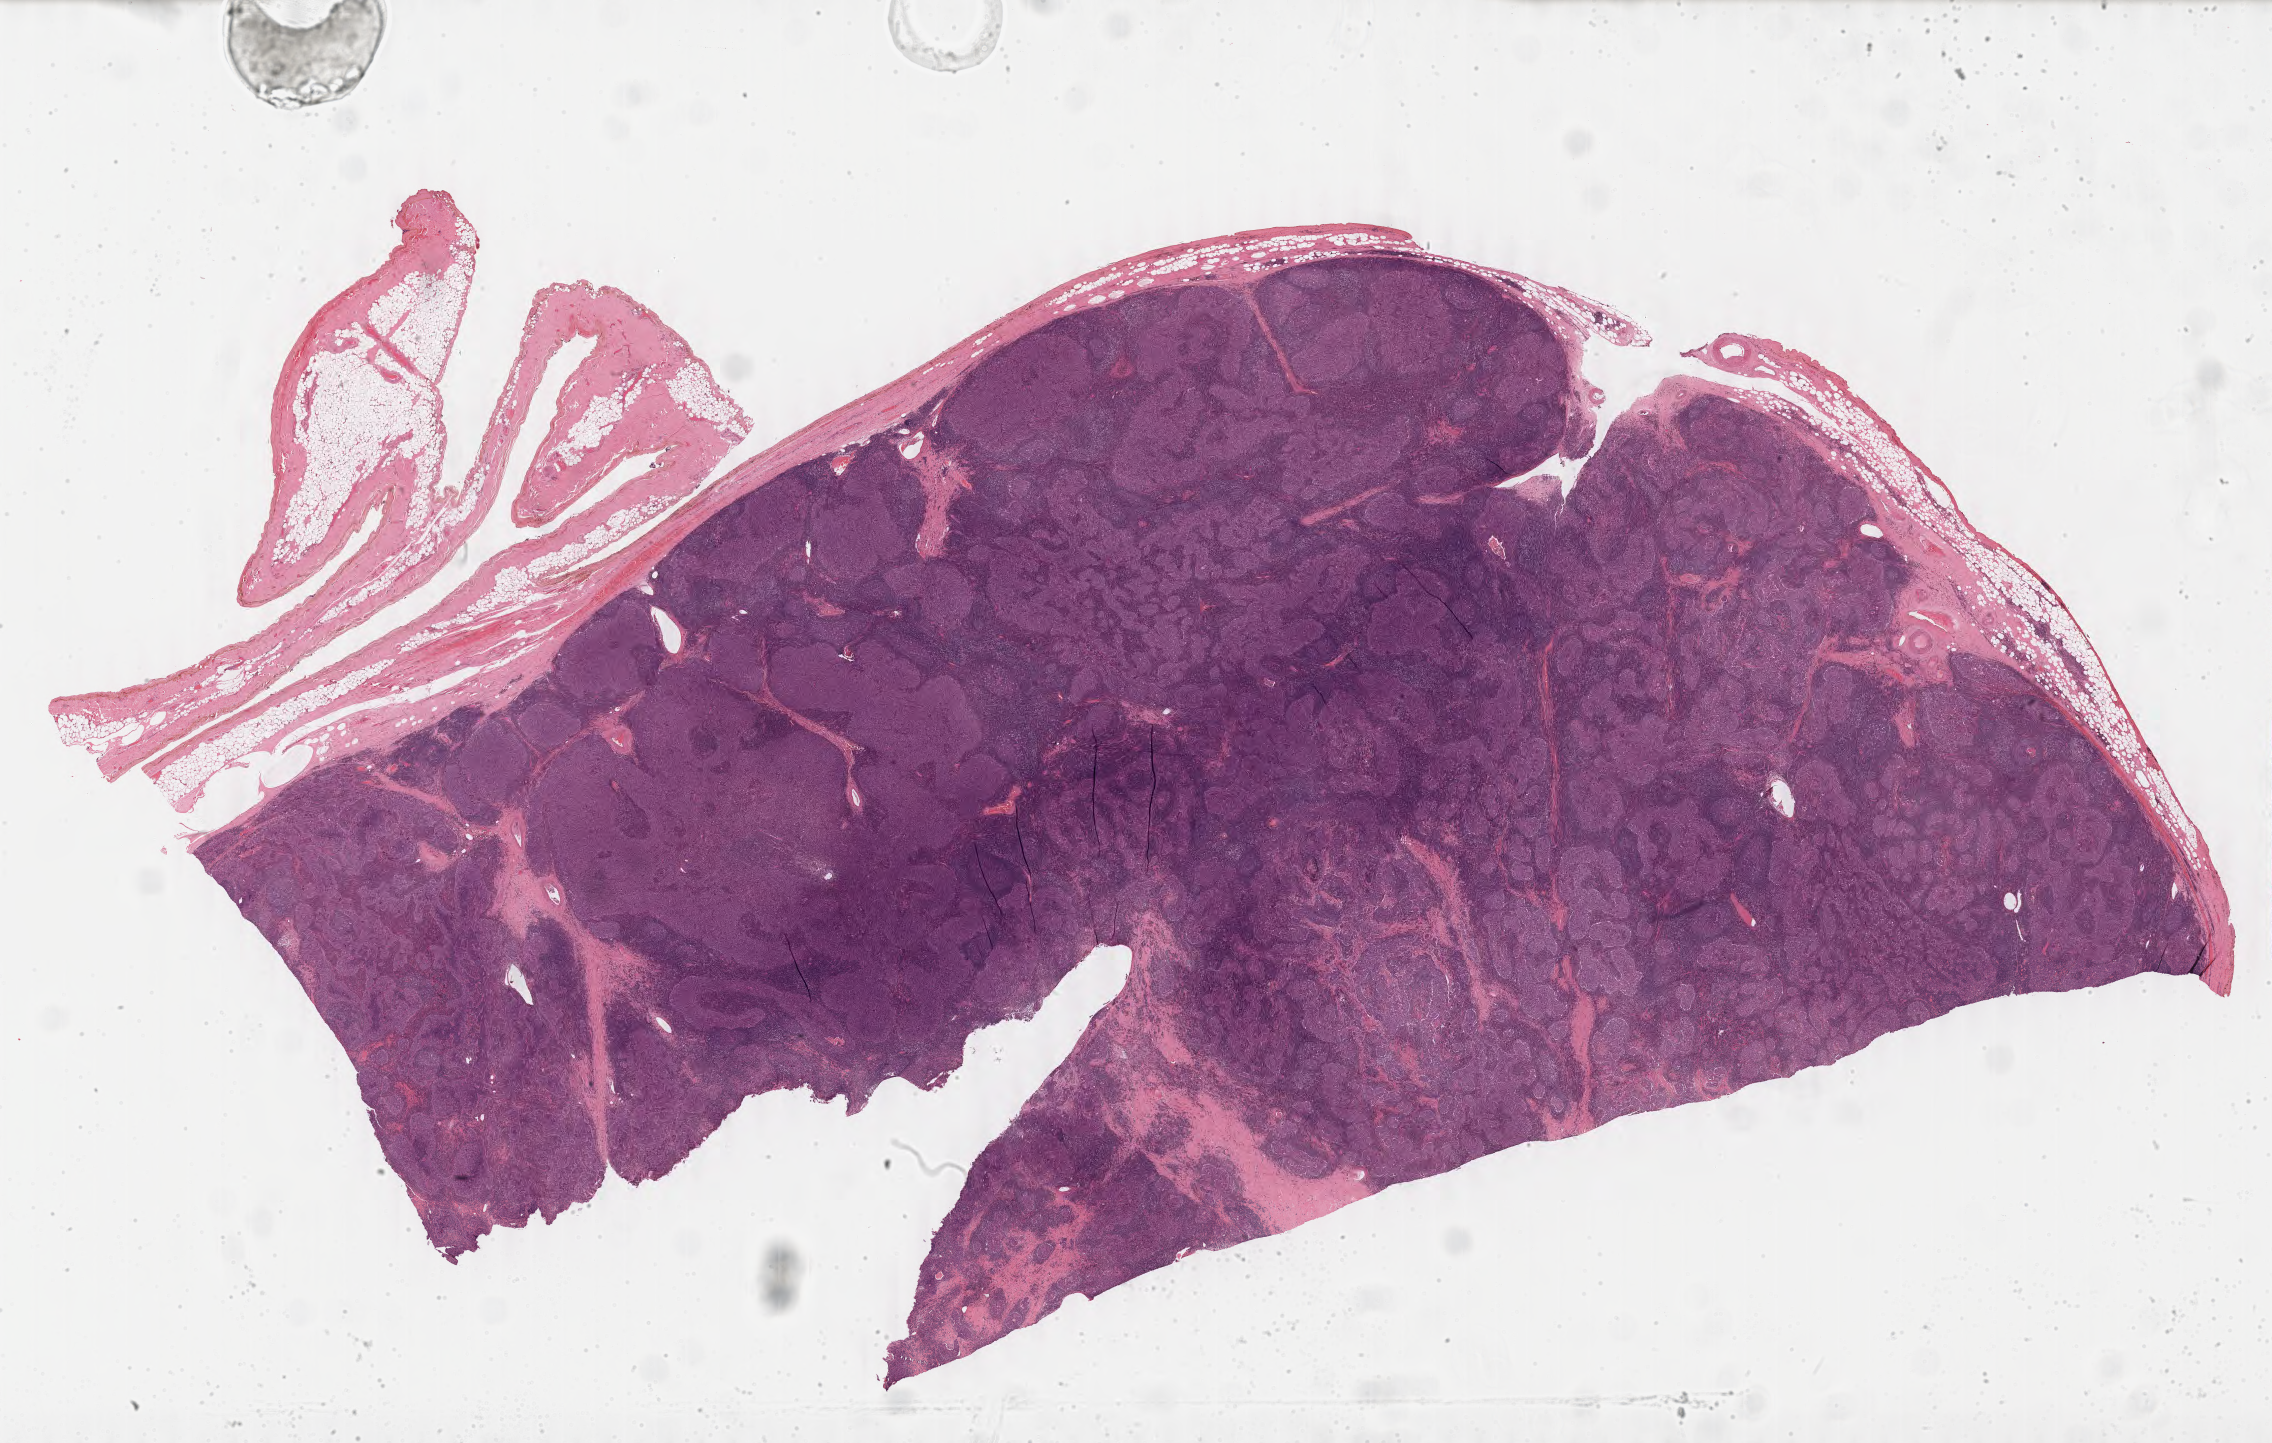
Whole-slide histology image, H&E — a low-resolution overview of the entire scanned area, about 35.9 x 22.8 mm (acquisition: 40x scan), formalin-fixed paraffin-embedded (FFPE) diagnostic section, thymus, primary tumour sample. Female, age 65 years at initial diagnosis.
• histologic diagnosis: Thymic carcinoma, NOS